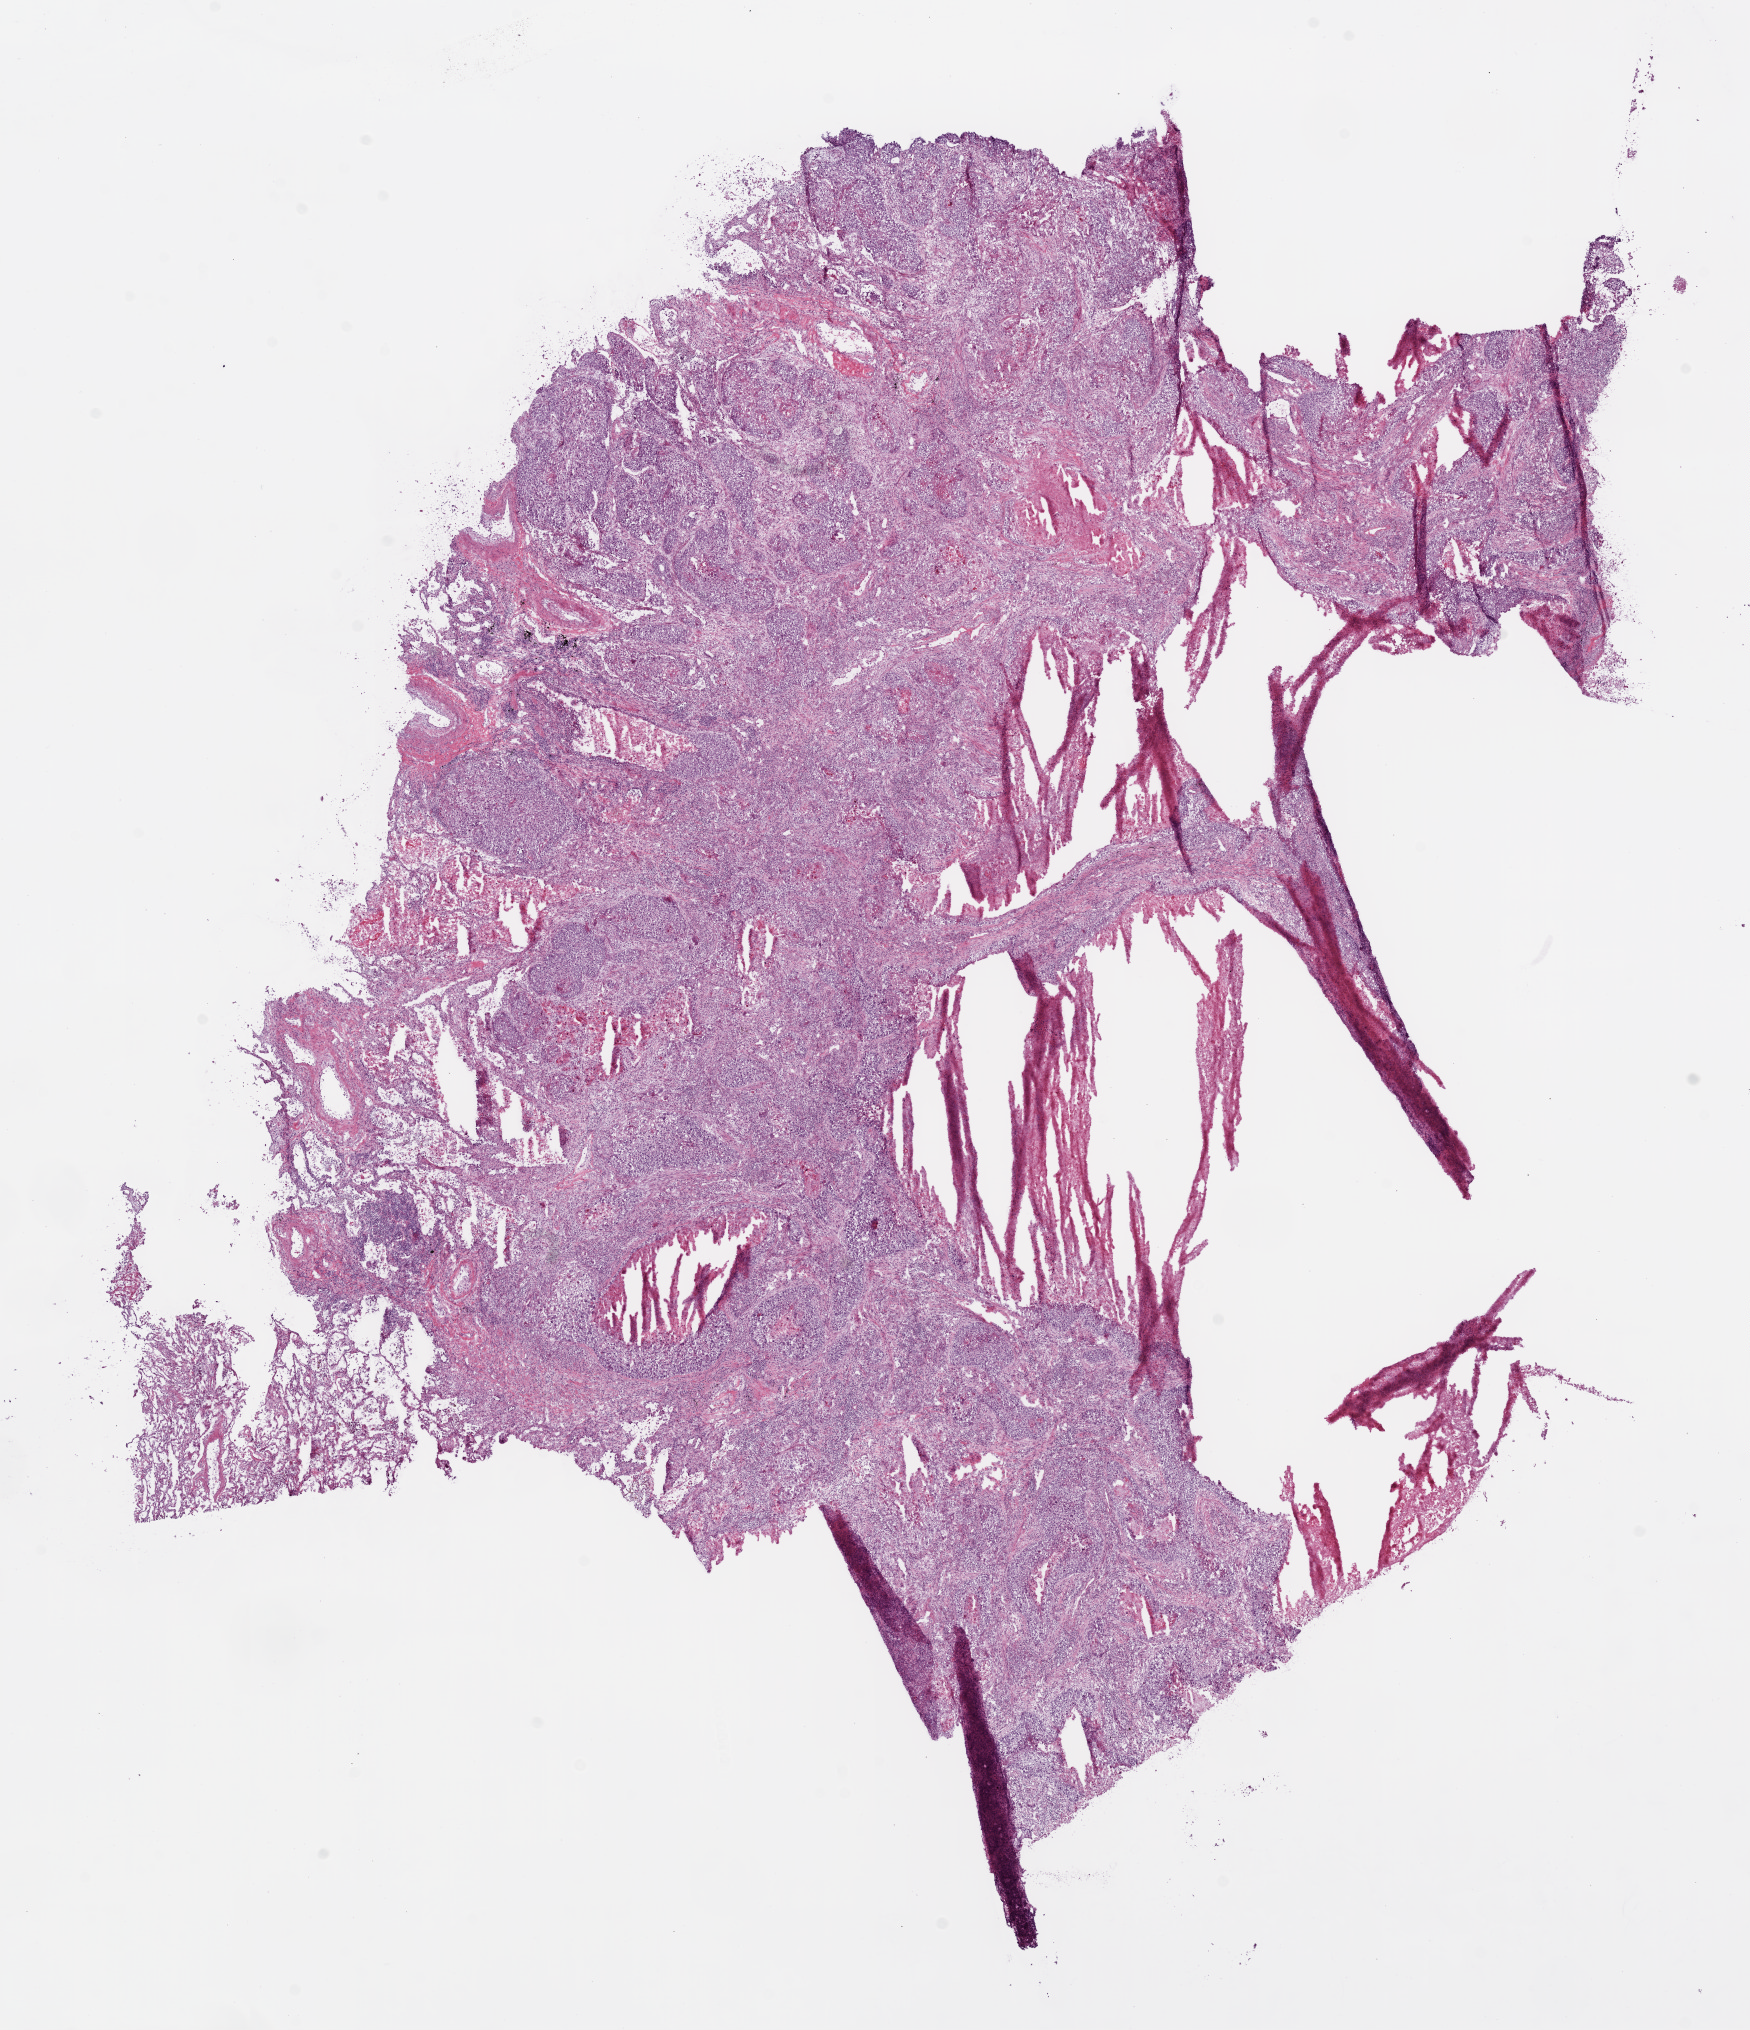
Whole-slide histology image, H&E — whole scanned area (about 14.0 x 16.3 mm) shown as a low-resolution overview, frozen section from the top of the tissue portion, lung, primary tumour sample. Male, age 79 years at initial diagnosis. Composition of this section per pathologist review: tumour cells 57%, tumour nuclei 75%, normal cells 3%, stromal cells 15%, necrosis 25%.
- pathologic diagnosis: Squamous cell carcinoma, NOS (lower lobe, lung)
- AJCC pathologic stage: IB
- laterality: right